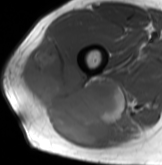
MRI of an extremity soft-tissue mass, one axial slice; slice 57 of 61 in the series (ordered by position); MR volume resampled by the dataset authors to the PET/CT grid (not the native acquisition matrix); 3.27 mm slice thickness; 162 × 165 image matrix, field of view 158 × 161 mm. Male patient. Case-level facts recorded for this patient, not image findings: histological type: poorly differentiated synovial sarcoma; grade: high; site of the primary tumour: right buttock.
Outlined on this slice (expert contour drawn on MRI and transferred to this co-registered scan by the dataset authors):
- gross tumour volume including surrounding oedema: bounding box (x1, y1, x2, y2) in pixels: (18, 36, 138, 146)
- gross tumour volume (mass): (20, 36, 126, 146)